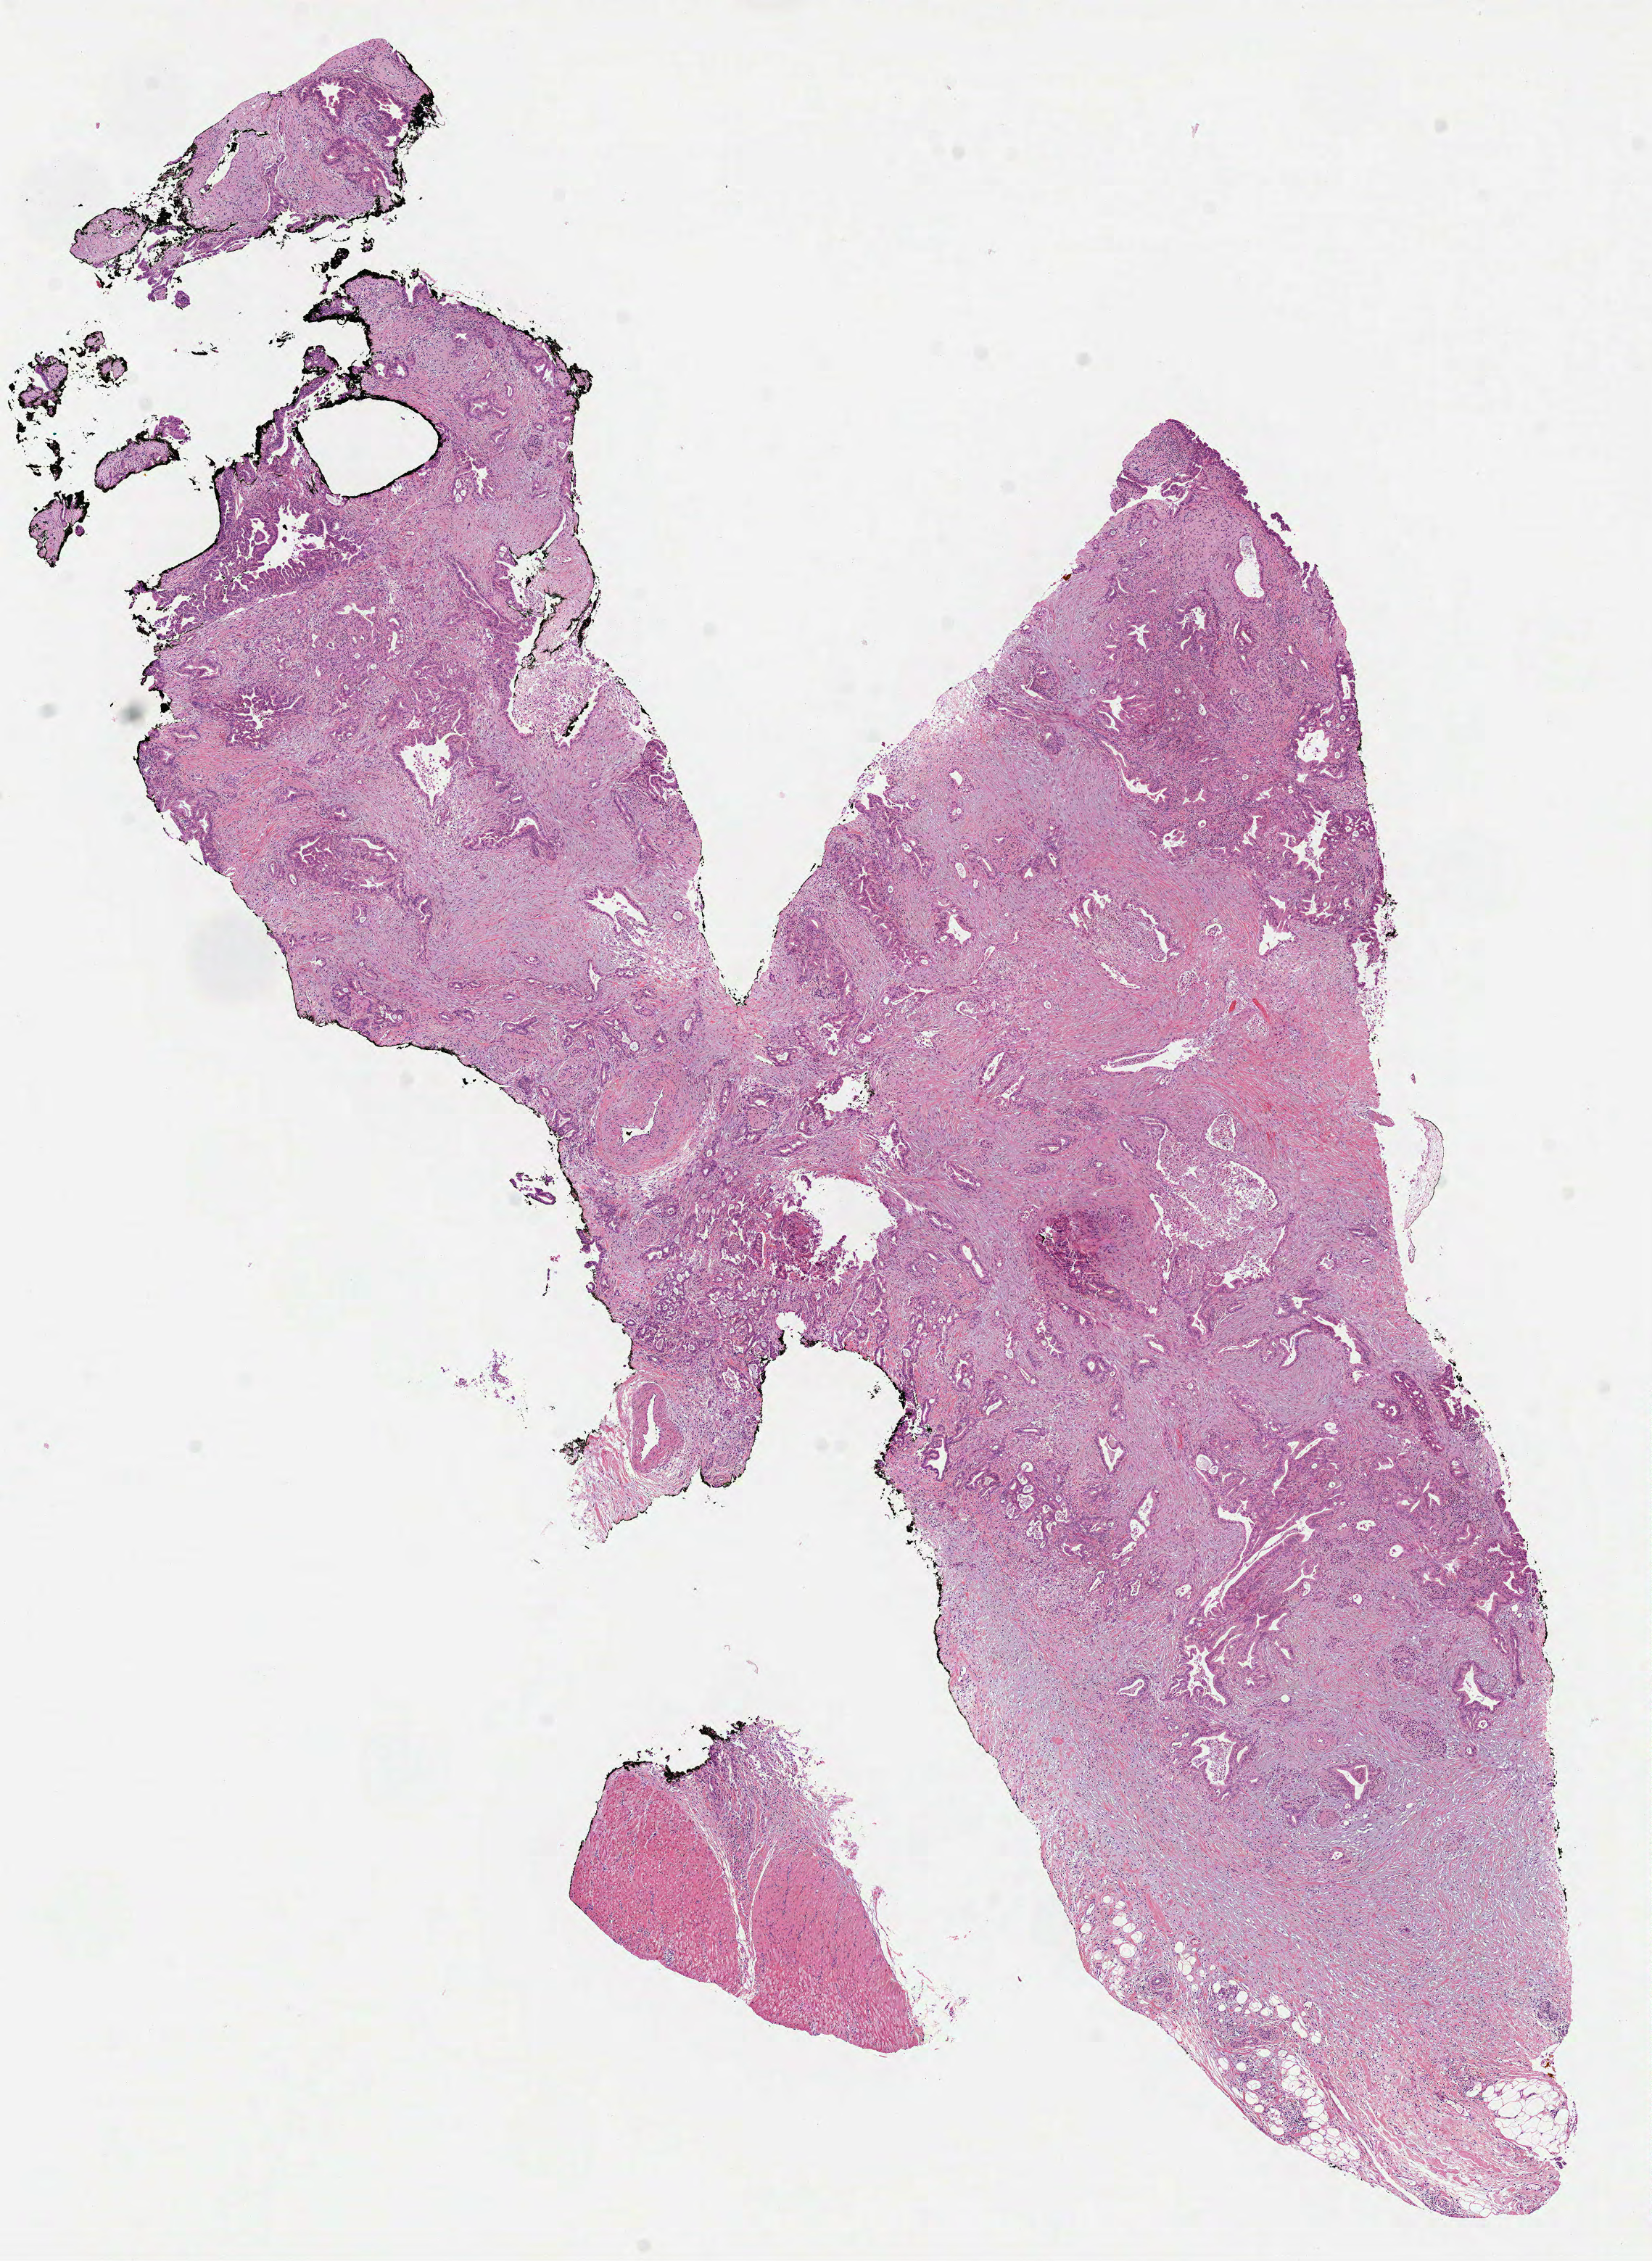
Digitized Hematoxylin and eosin (H&E) stained tissue section (whole slide), a low-resolution overview of the entire scanned area, about 9.2 x 12.6 mm (acquisition: 40x scan), formalin-fixed paraffin-embedded (FFPE) diagnostic section, sample: primary tumour, pancreas. Female patient; age at initial diagnosis 52 years. Histologic grade: G2 (moderately differentiated).
TNM: T3 N1 M0. Lymph nodes positive (case pathology): 2 of 10 examined. AJCC pathologic stage: IIB. Diagnosis: Infiltrating duct carcinoma, NOS (head of pancreas).